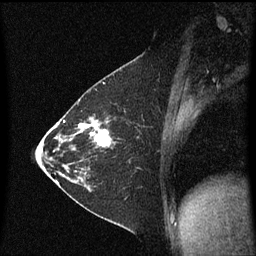
Breast MRI (dynamic contrast-enhanced), one sagittal slice; slice 31 of 60 in the series (ordered by position); dynamic contrast-enhanced series, image 2 of 3 at this slice position (ordered by acquisition); 1.5 T; TE 4.2 ms, TR 8.4 ms; 2 mm slice thickness; 256 × 256 image matrix. Patient: female, 36 years. From the clinical record (not read from this slice): setting: breast cancer imaged before/during neoadjuvant chemotherapy; receptor status: HR-positive, HER2-negative.
Annotated regions visible in this slice (semi-automatically segmented with operator editing):
- analysis volume of interest (the breast-tissue region the enhancement analysis was run in; not a lesion): box from (x=72, y=116) to (x=117, y=187) px
- tumour enhancement mask (voxels above the 70 % enhancement threshold inside the analysis volume of interest): (x=76, y=120)–(x=113, y=183)